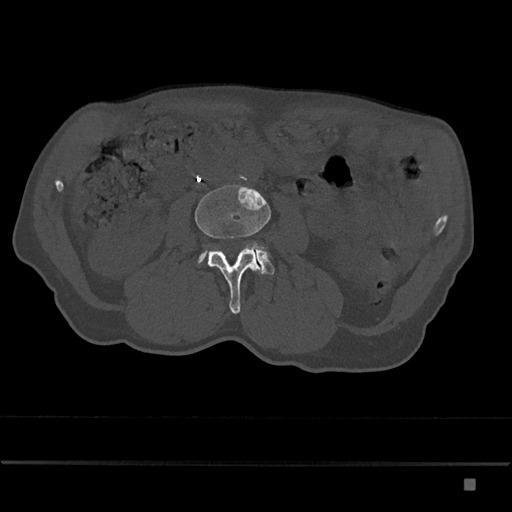
CT including the spine, one axial slice; reconstruction kernel Br40s/3; bone window (W 1800 / L 400 HU); 0.5 mm slice thickness; 512 × 512 image matrix. Patient: male, 72 years. Case-level facts recorded for this patient, not image findings: primary cancer: prostate.
Structures marked on this image (semi-automatically segmented with operator editing):
- L3 vertebra: bounding box (x1, y1, x2, y2) in pixels: (195, 185, 271, 314)
- L4 vertebra: (198, 244, 274, 275)